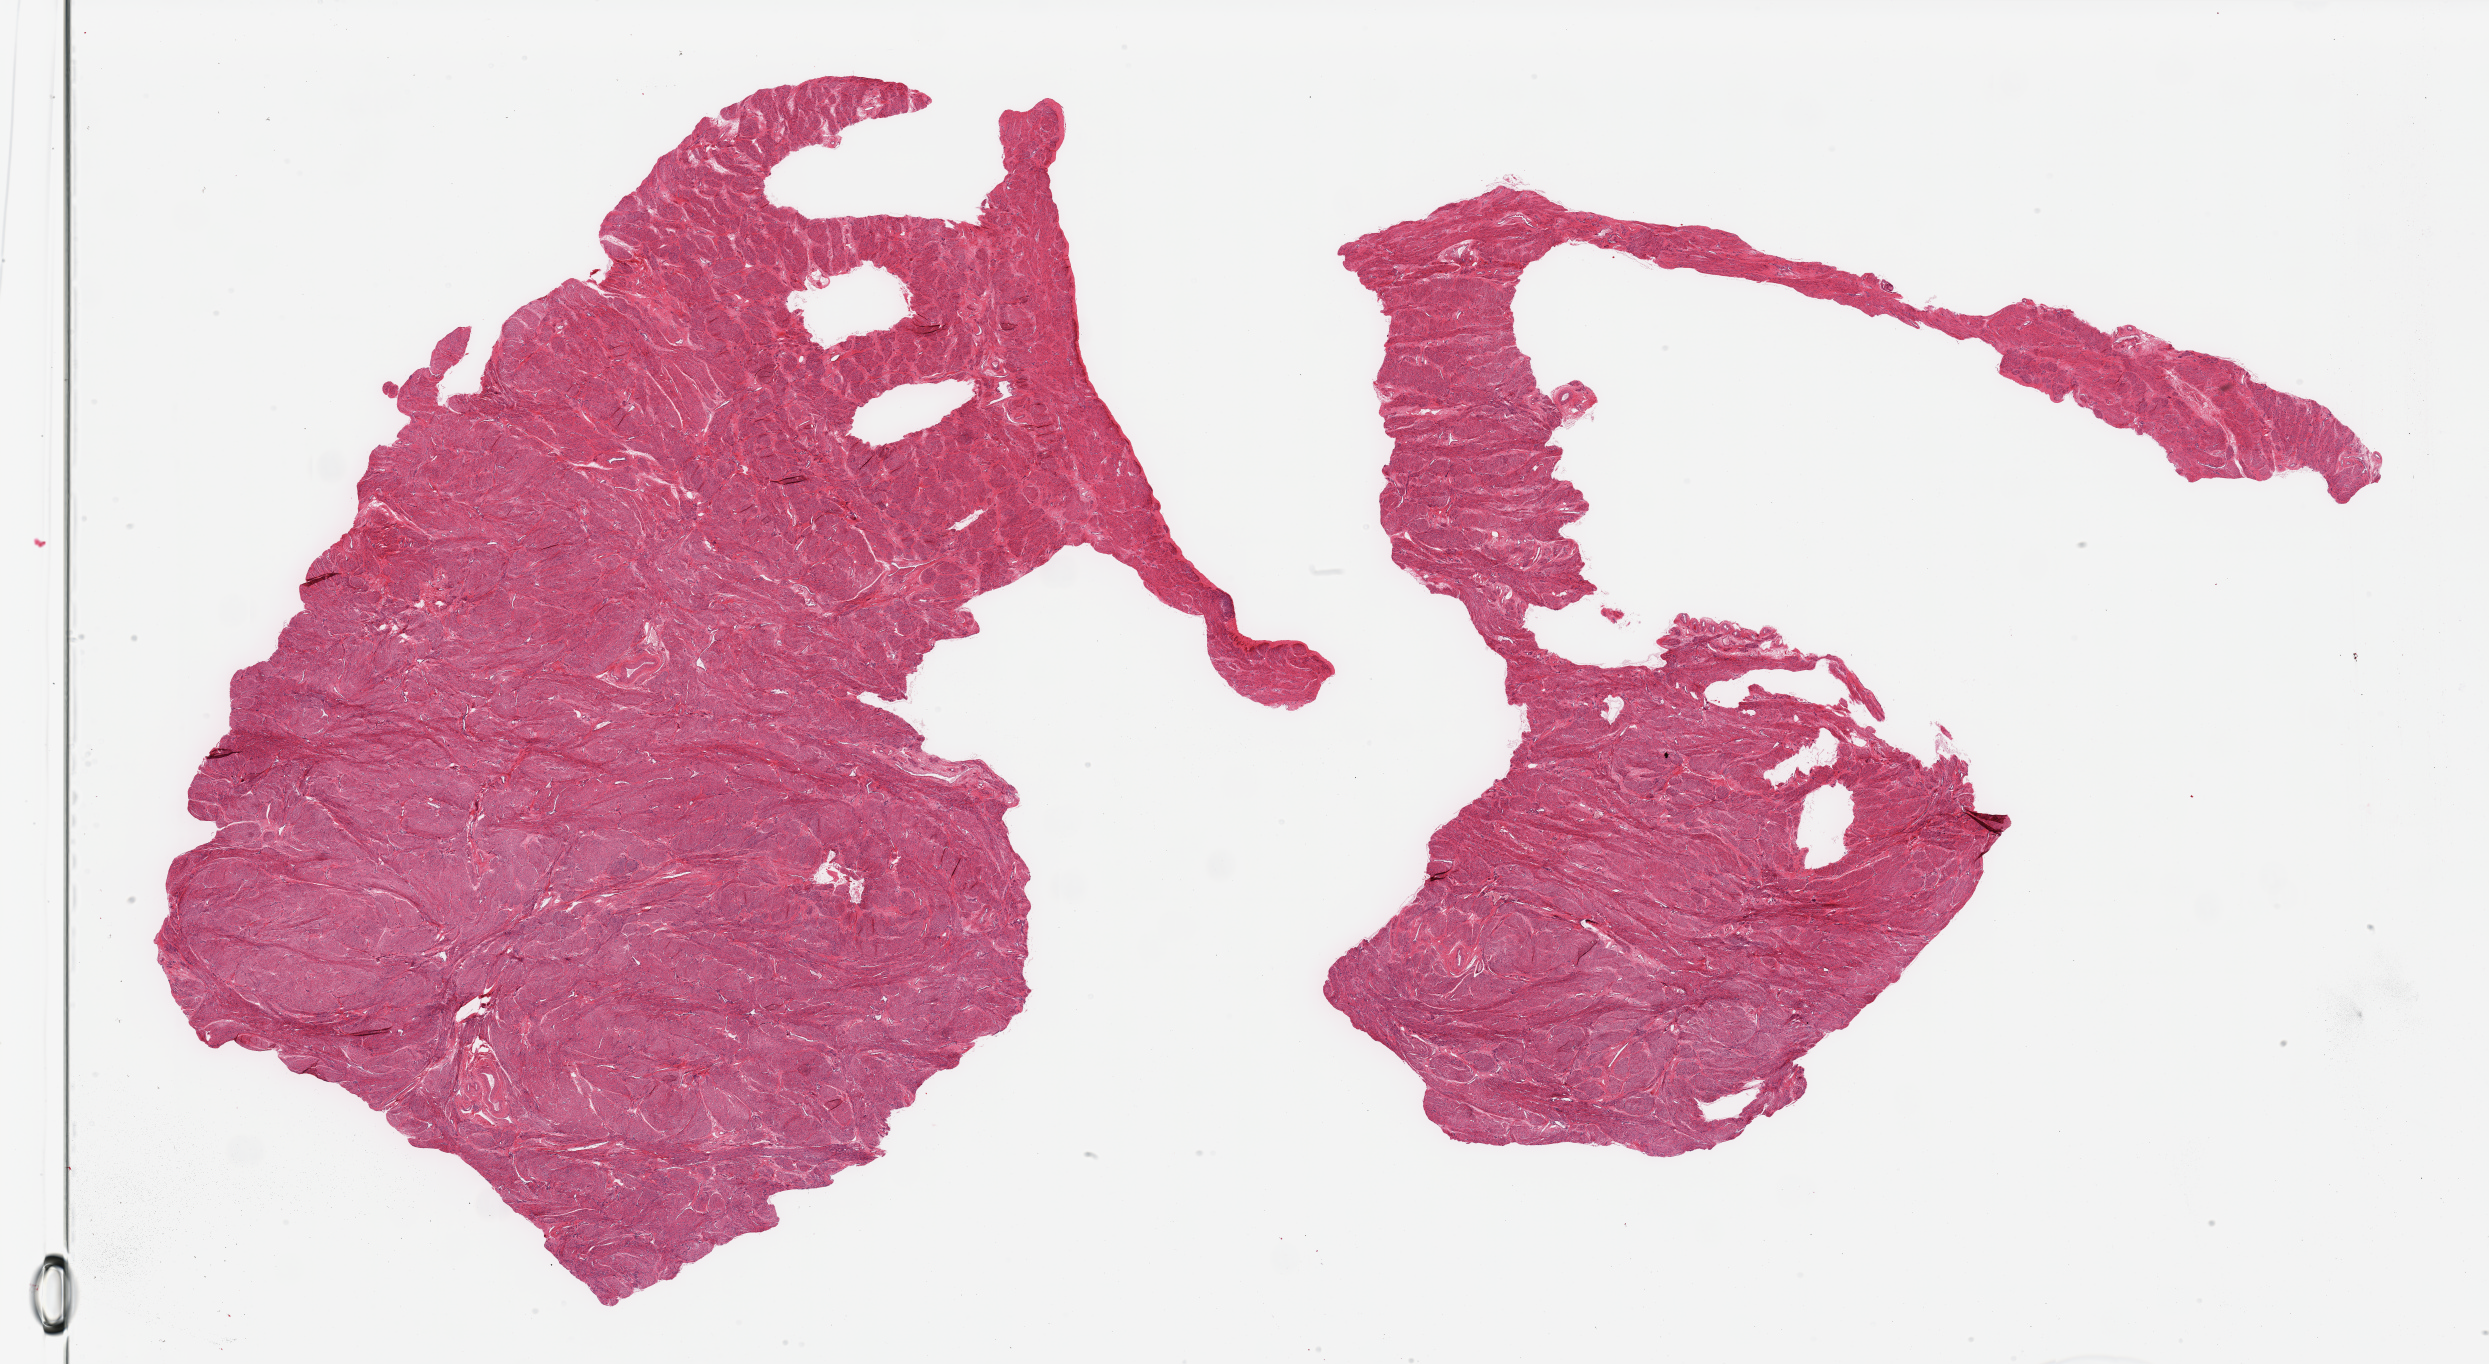
Digitized haematoxylin and eosin-stained section — a low-resolution overview of the entire scanned area, about 39.4 x 21.6 mm. PAXgene-fixed paraffin-embedded (PFPE) section. Section of uterus (target tissue). Tissue donor sample. Female donor.
Pathologist's review note for this sample: 2 pieces; myometrium only in this section.